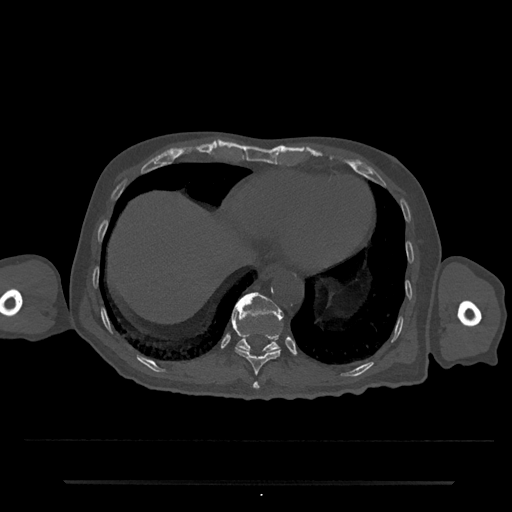
CT including the spine, one axial slice; slice 293 of 797 in the series (ordered by position); reconstruction kernel Br40s/3; bone window (W 1800 / L 400 HU); 512 × 512 image matrix. Patient: male, 74 years. From the clinical record (not read from this slice): primary cancer: prostate.
Annotated regions visible in this slice (semi-automatic segmentation, software-assisted and operator-edited):
- T10 vertebra: bounding box (x1, y1, x2, y2) in pixels: (231, 315, 282, 375)
- T11 vertebra: (232, 292, 284, 353)
- T9 vertebra: (252, 382, 260, 389)